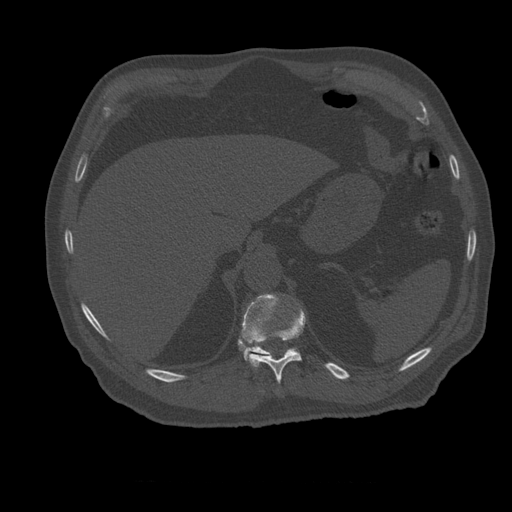
CT including the spine, one axial slice. Slice 276 of 399 in the series (ordered by position). Reconstruction kernel STANDARD. Bone window (W 1800 / L 400 HU). 512 × 512 image matrix, field of view 407 × 407 mm. Patient age 73 years. Case-level facts recorded for this patient, not image findings: primary cancer: prostate; vertebrae with lytic lesions (as recorded): L2.
Outlined on this slice (semi-automatic segmentation, software-assisted and operator-edited):
- T11 vertebra: bounding box [x1, y1, x2, y2] px = [249, 309, 306, 384]
- T12 vertebra: [240, 294, 298, 362]